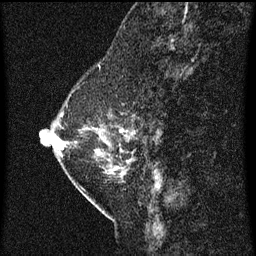
Breast MRI (dynamic contrast-enhanced), one sagittal slice. Dynamic contrast-enhanced series, image 2 of 3 at this slice position (ordered by acquisition). 1.5 T. TE 4.2 ms, TR 8 ms. 2 mm slice thickness. 256 × 256 image matrix, field of view 180 × 180 mm. Patient: female, 47 years.
Outlined on this slice (semi-automatic segmentation, software-assisted and operator-edited):
- analysis volume of interest (the breast-tissue region the enhancement analysis was run in; not a lesion): bounding box <54,84,140,187> (left, top, right, bottom; pixels)
- tumour enhancement mask (voxels above the 70 % enhancement threshold inside the analysis volume of interest): <62,132,134,157>